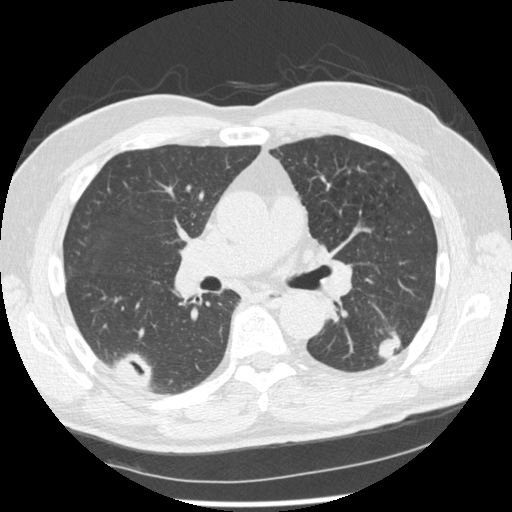
Axial slice from a low-dose chest CT screening exam, second screening round (one year after baseline), lung window (W 1500 / L -600 HU), slice 110 of 227 in the series, 512 × 512 image matrix, field of view 360 × 360 mm. Male, age 74 years at enrolment. Former smoker at enrolment.
• Expert-annotated lung lesion, box from (x=371, y=316) to (x=421, y=368) px.
• The screening reader recorded 7 non-calcified nodules or masses ≥4 mm on this exam (right upper lobe, right lower lobe, right upper lobe, right lower lobe, left lower lobe, left upper lobe, left upper lobe); which of them this box marks is not recorded.